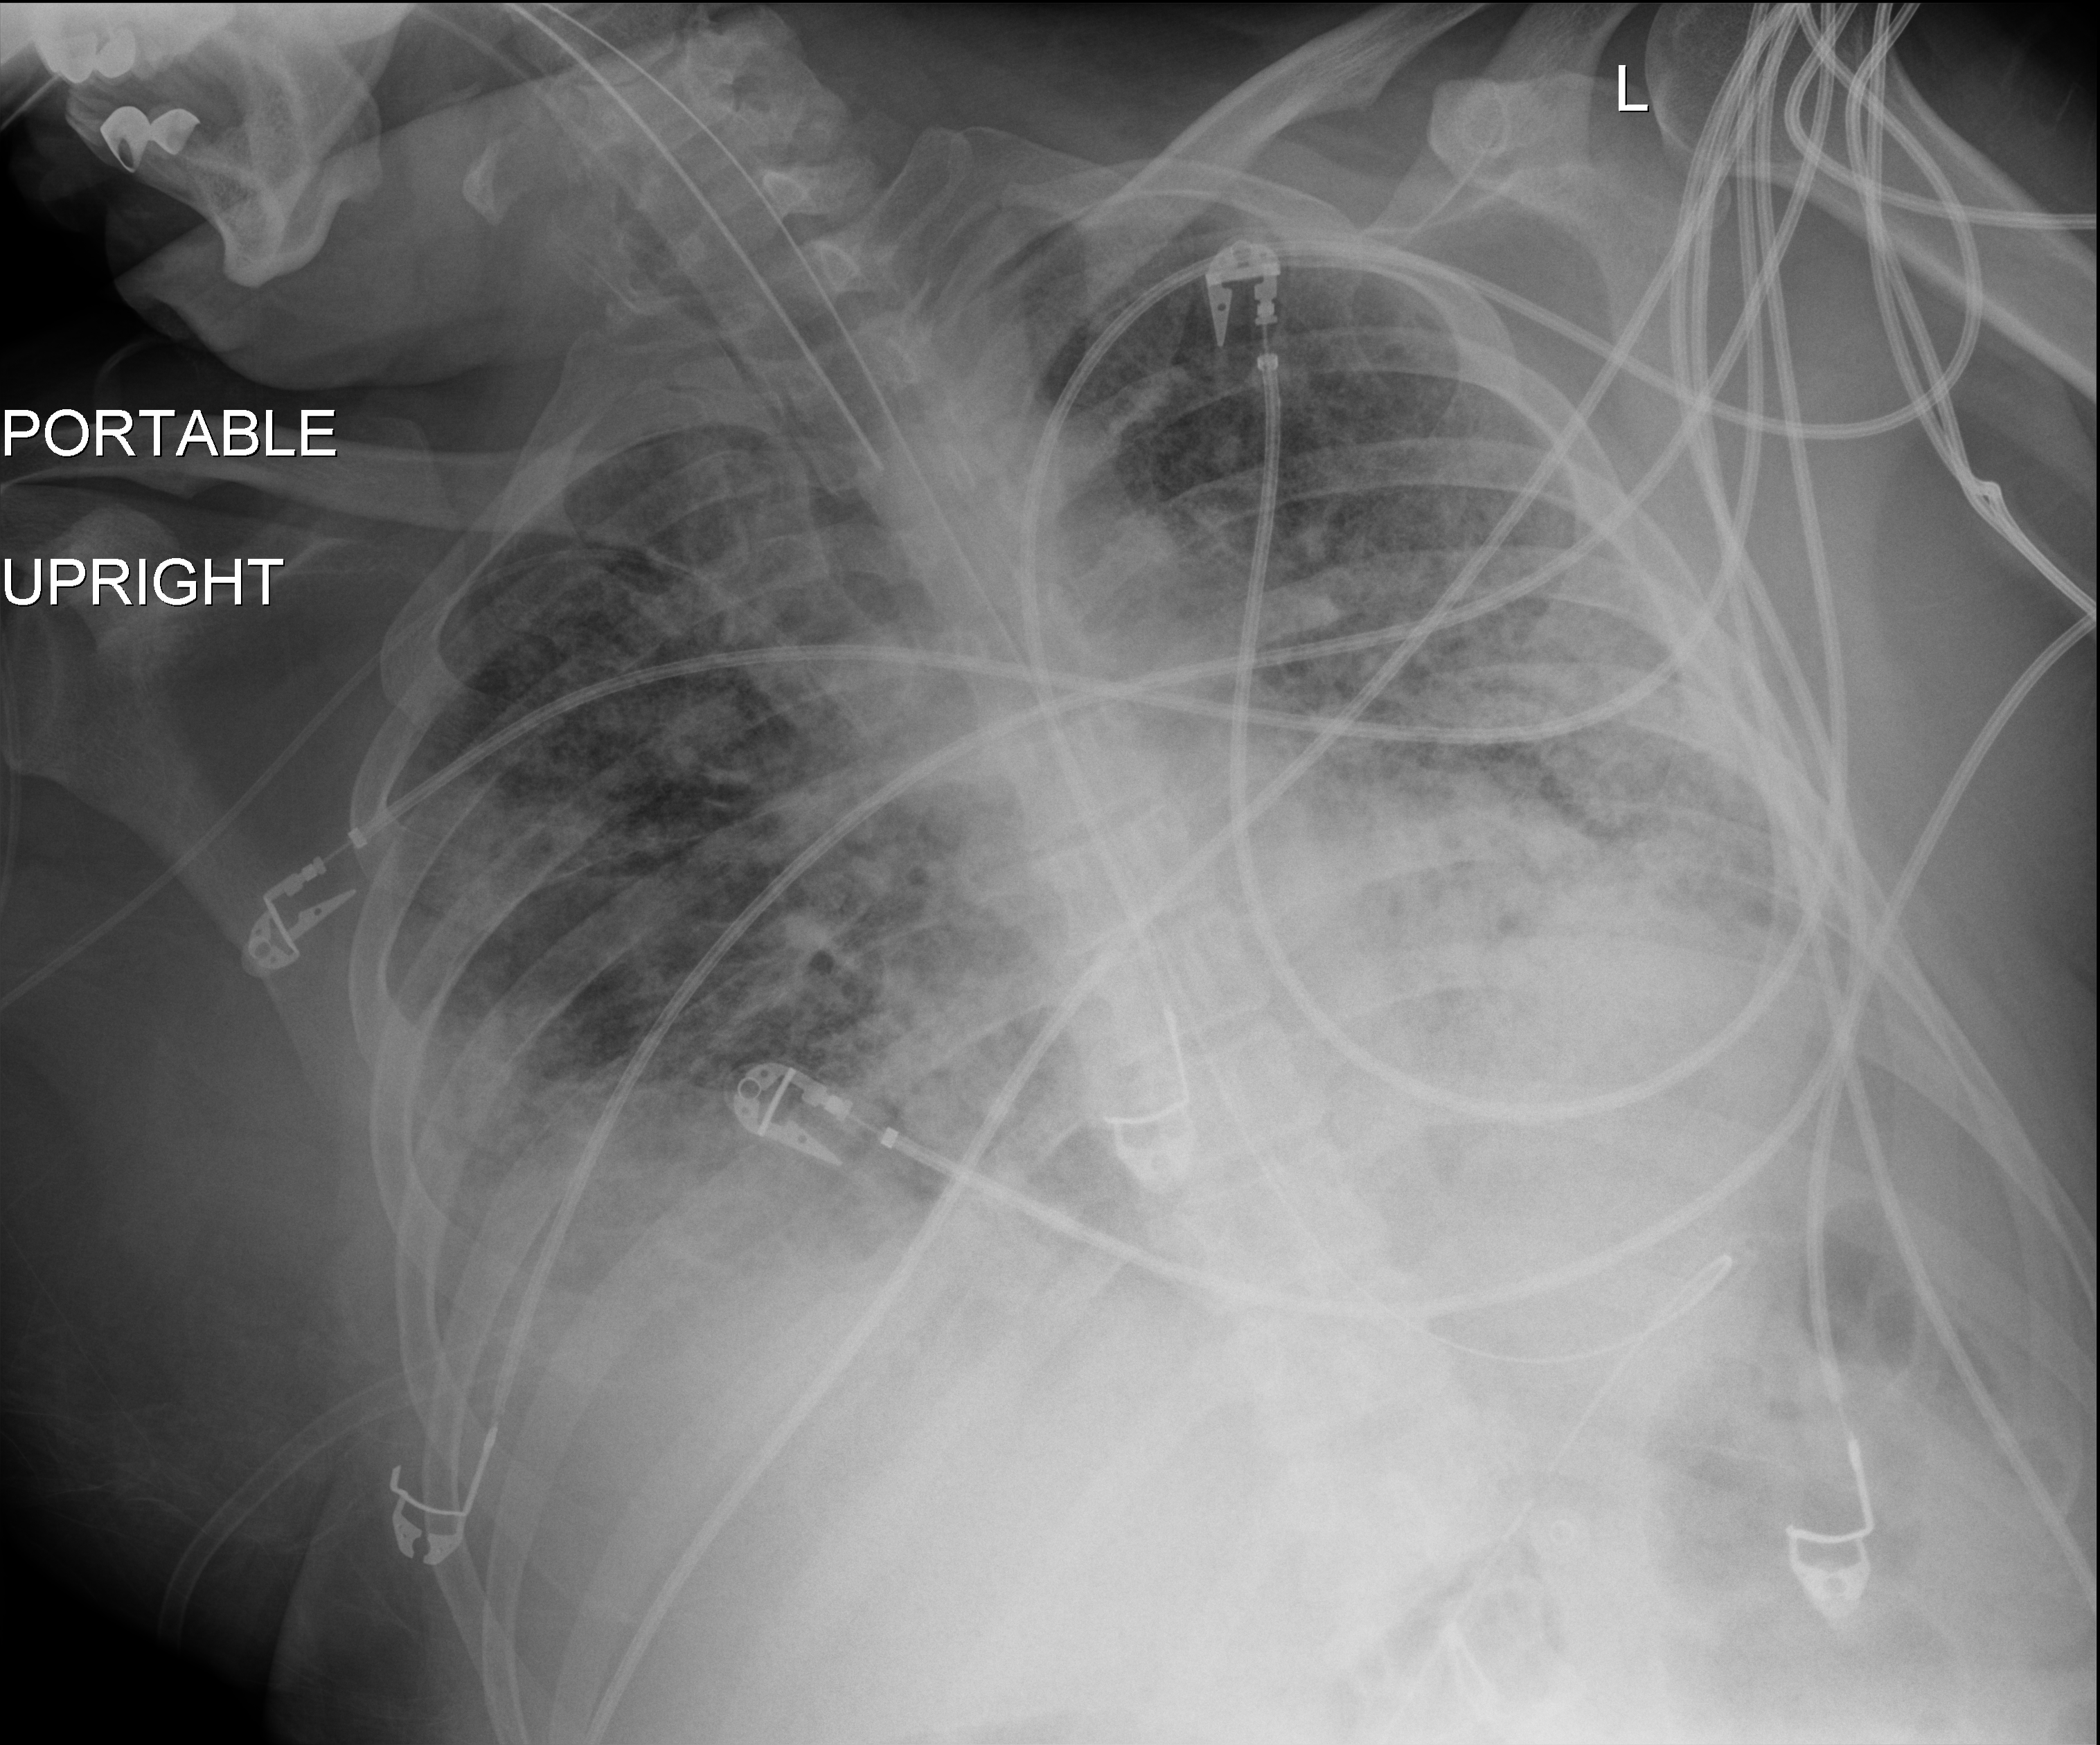
Bedside chest radiograph (digital radiography); anteroposterior (AP) projection. Patient hospitalised with COVID-19; male, aged 18–59 years.
Admission-level facts for this patient (not findings on this image; timing relative to this image not recorded): admitted to intensive care during this hospital stay: yes.